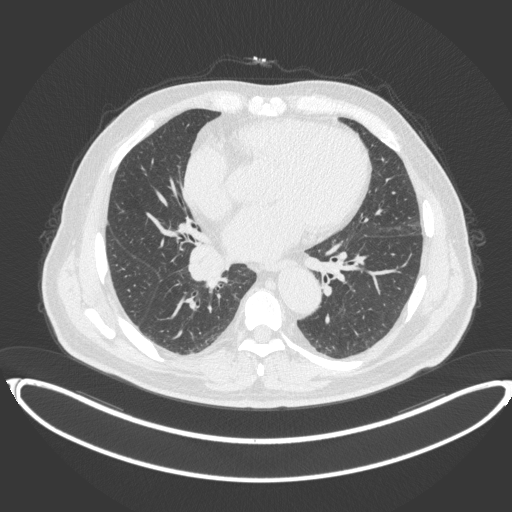
Chest CT, one axial slice; slice 186 of 383 in the series (ordered by position); lung window (W 1500 / L -600 HU); 512 × 512 image matrix, field of view 448 × 448 mm. Male patient, age 61 years. Case-level facts recorded for this patient, not image findings: clinical TNM (as recorded): T1b N1 M0.
Outlined on this slice (rectangle marked by the reading radiologist):
- lung tumour (recorded histology: squamous cell carcinoma): bounding box [x1, y1, x2, y2] px = [188, 242, 229, 290]